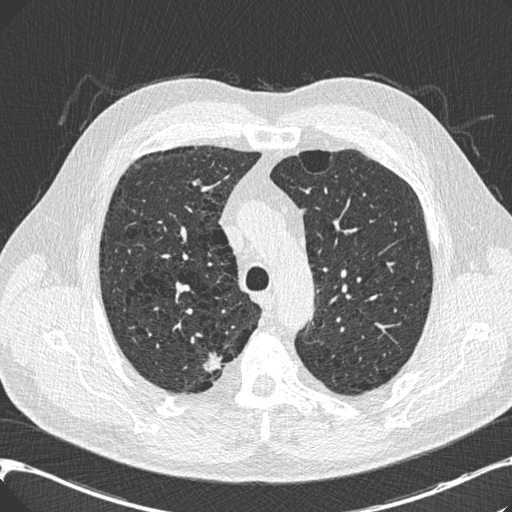
Low-dose screening chest CT, axial slice; third annual screen; lung window (W 1500 / L -600 HU); 0.75 mm slice thickness; standard (soft-tissue) reconstruction kernel (B30f); 120 kVp. Male participant, aged 68 years at enrolment.
• Expert reader's lesion annotation, box from (x=189, y=346) to (x=235, y=385) px.
• The screening reader recorded 3 non-calcified nodules or masses ≥4 mm on this exam; which of them this box marks is not recorded.
• Official screen result: positive, other.
• Later outcome: lung cancer diagnosed 46 days after this screen — adenocarcinoma, NOS, right upper lobe, well differentiated (G1), stage IB (AJCC 6th edition), 15 mm at pathology.